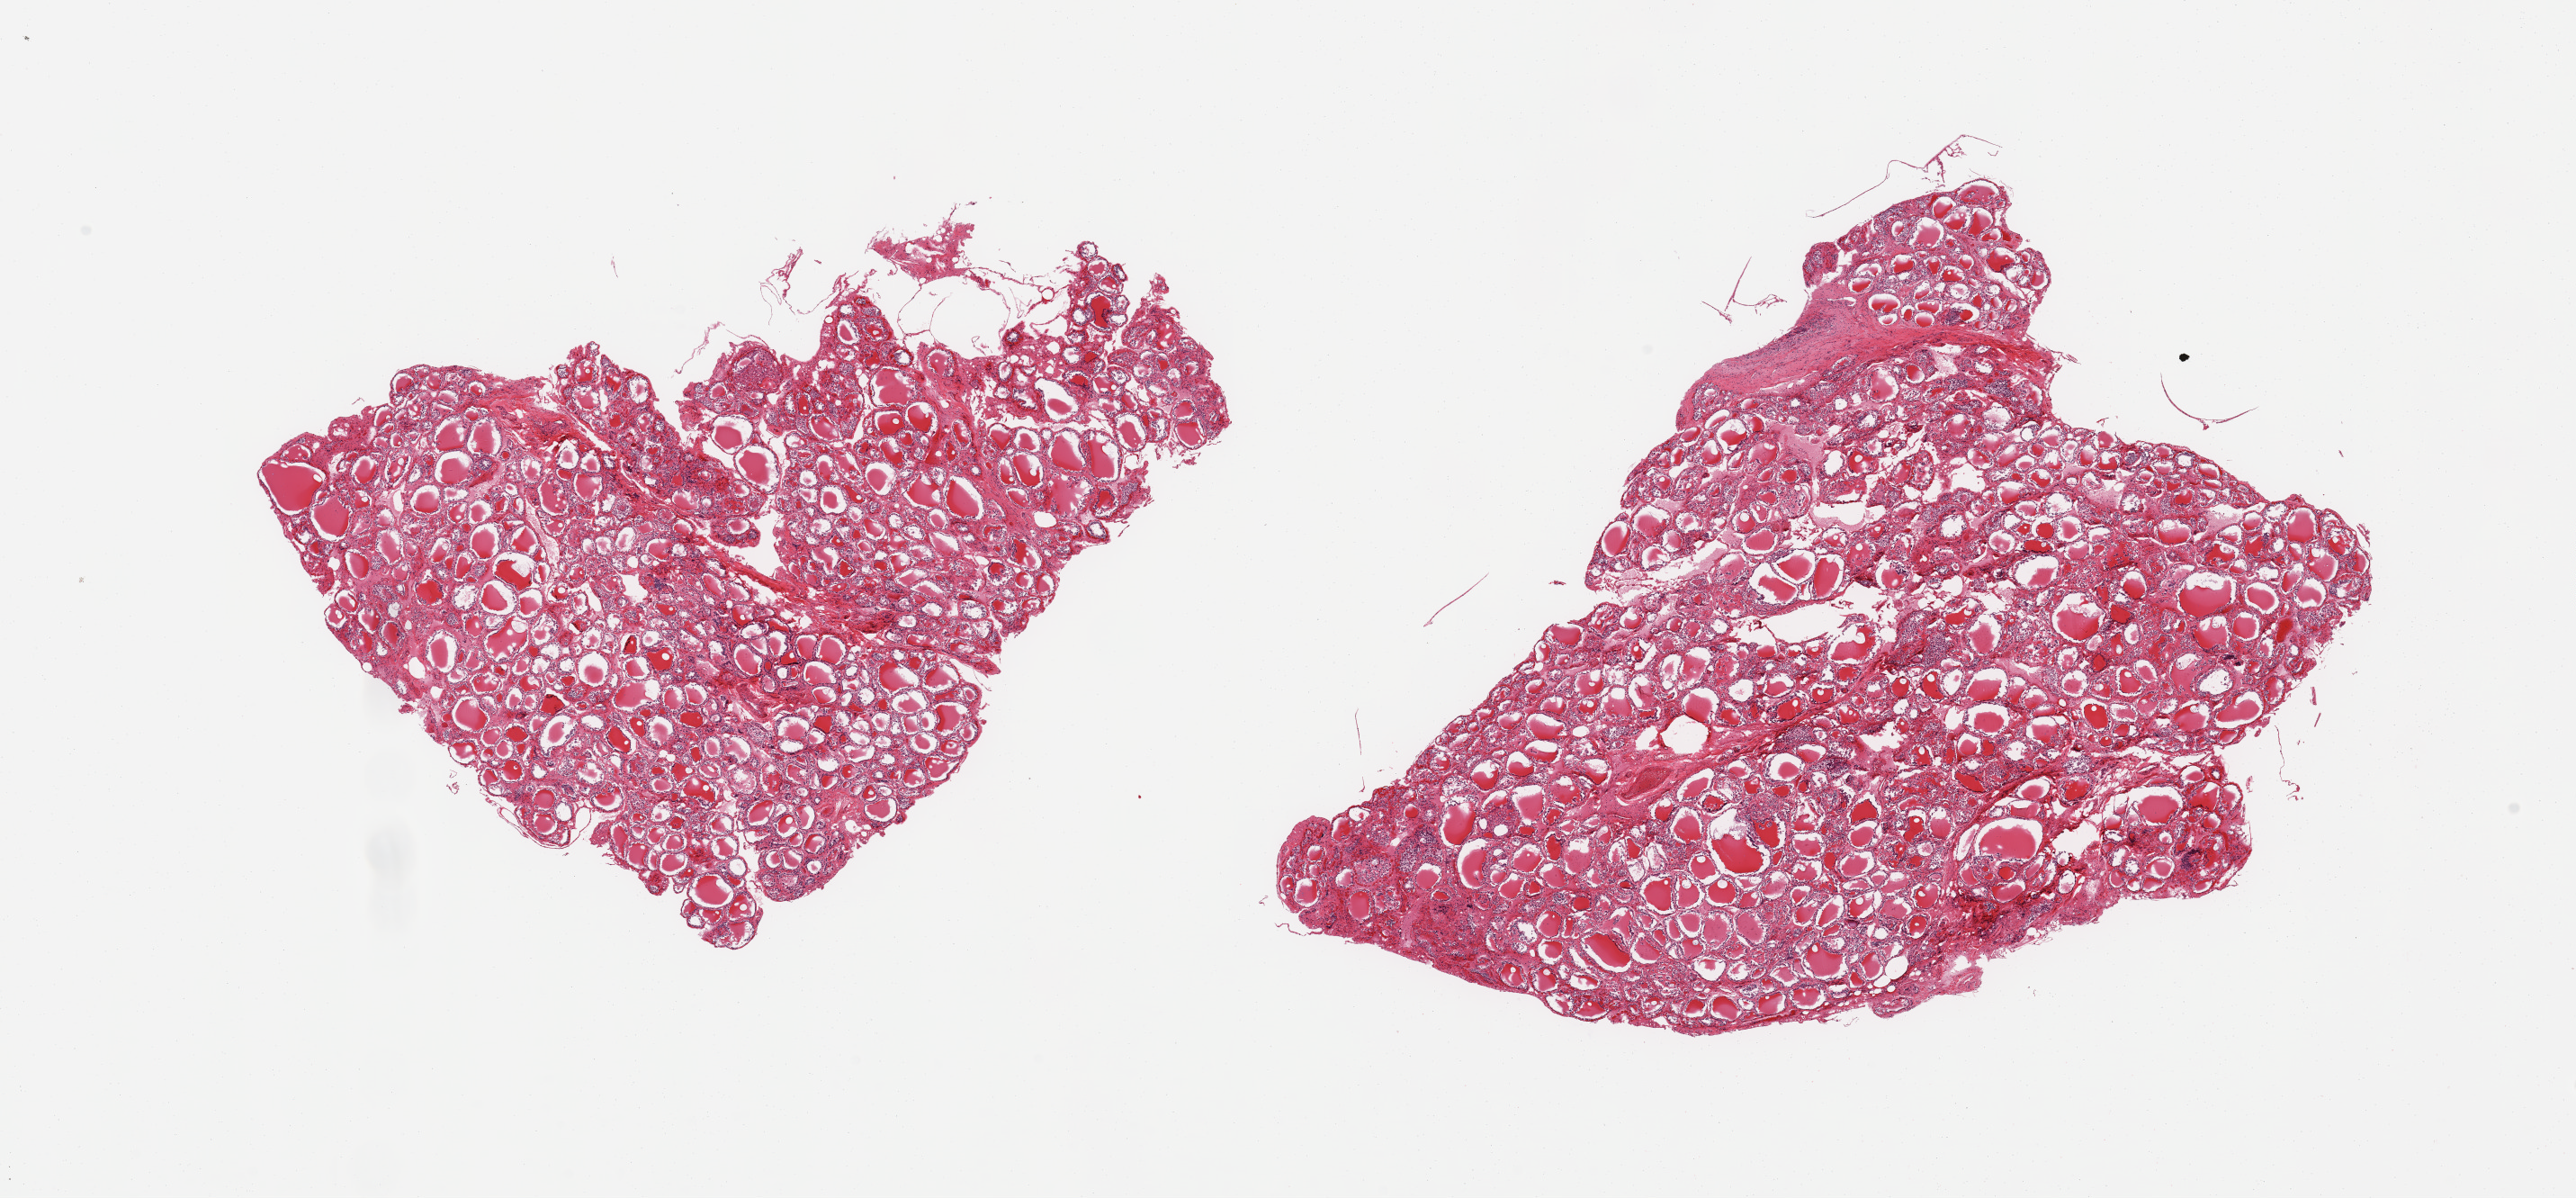
Digitized haematoxylin and eosin-stained section — low-resolution overview of the scanned area, about 22.6 x 10.5 mm (acquisition: 20x scan), PAXgene-fixed, paraffin-embedded tissue, section of thyroid (target tissue), tissue donor sample. Male donor.
- pathologist's review note for this sample: 2 pieces, no abnormalities